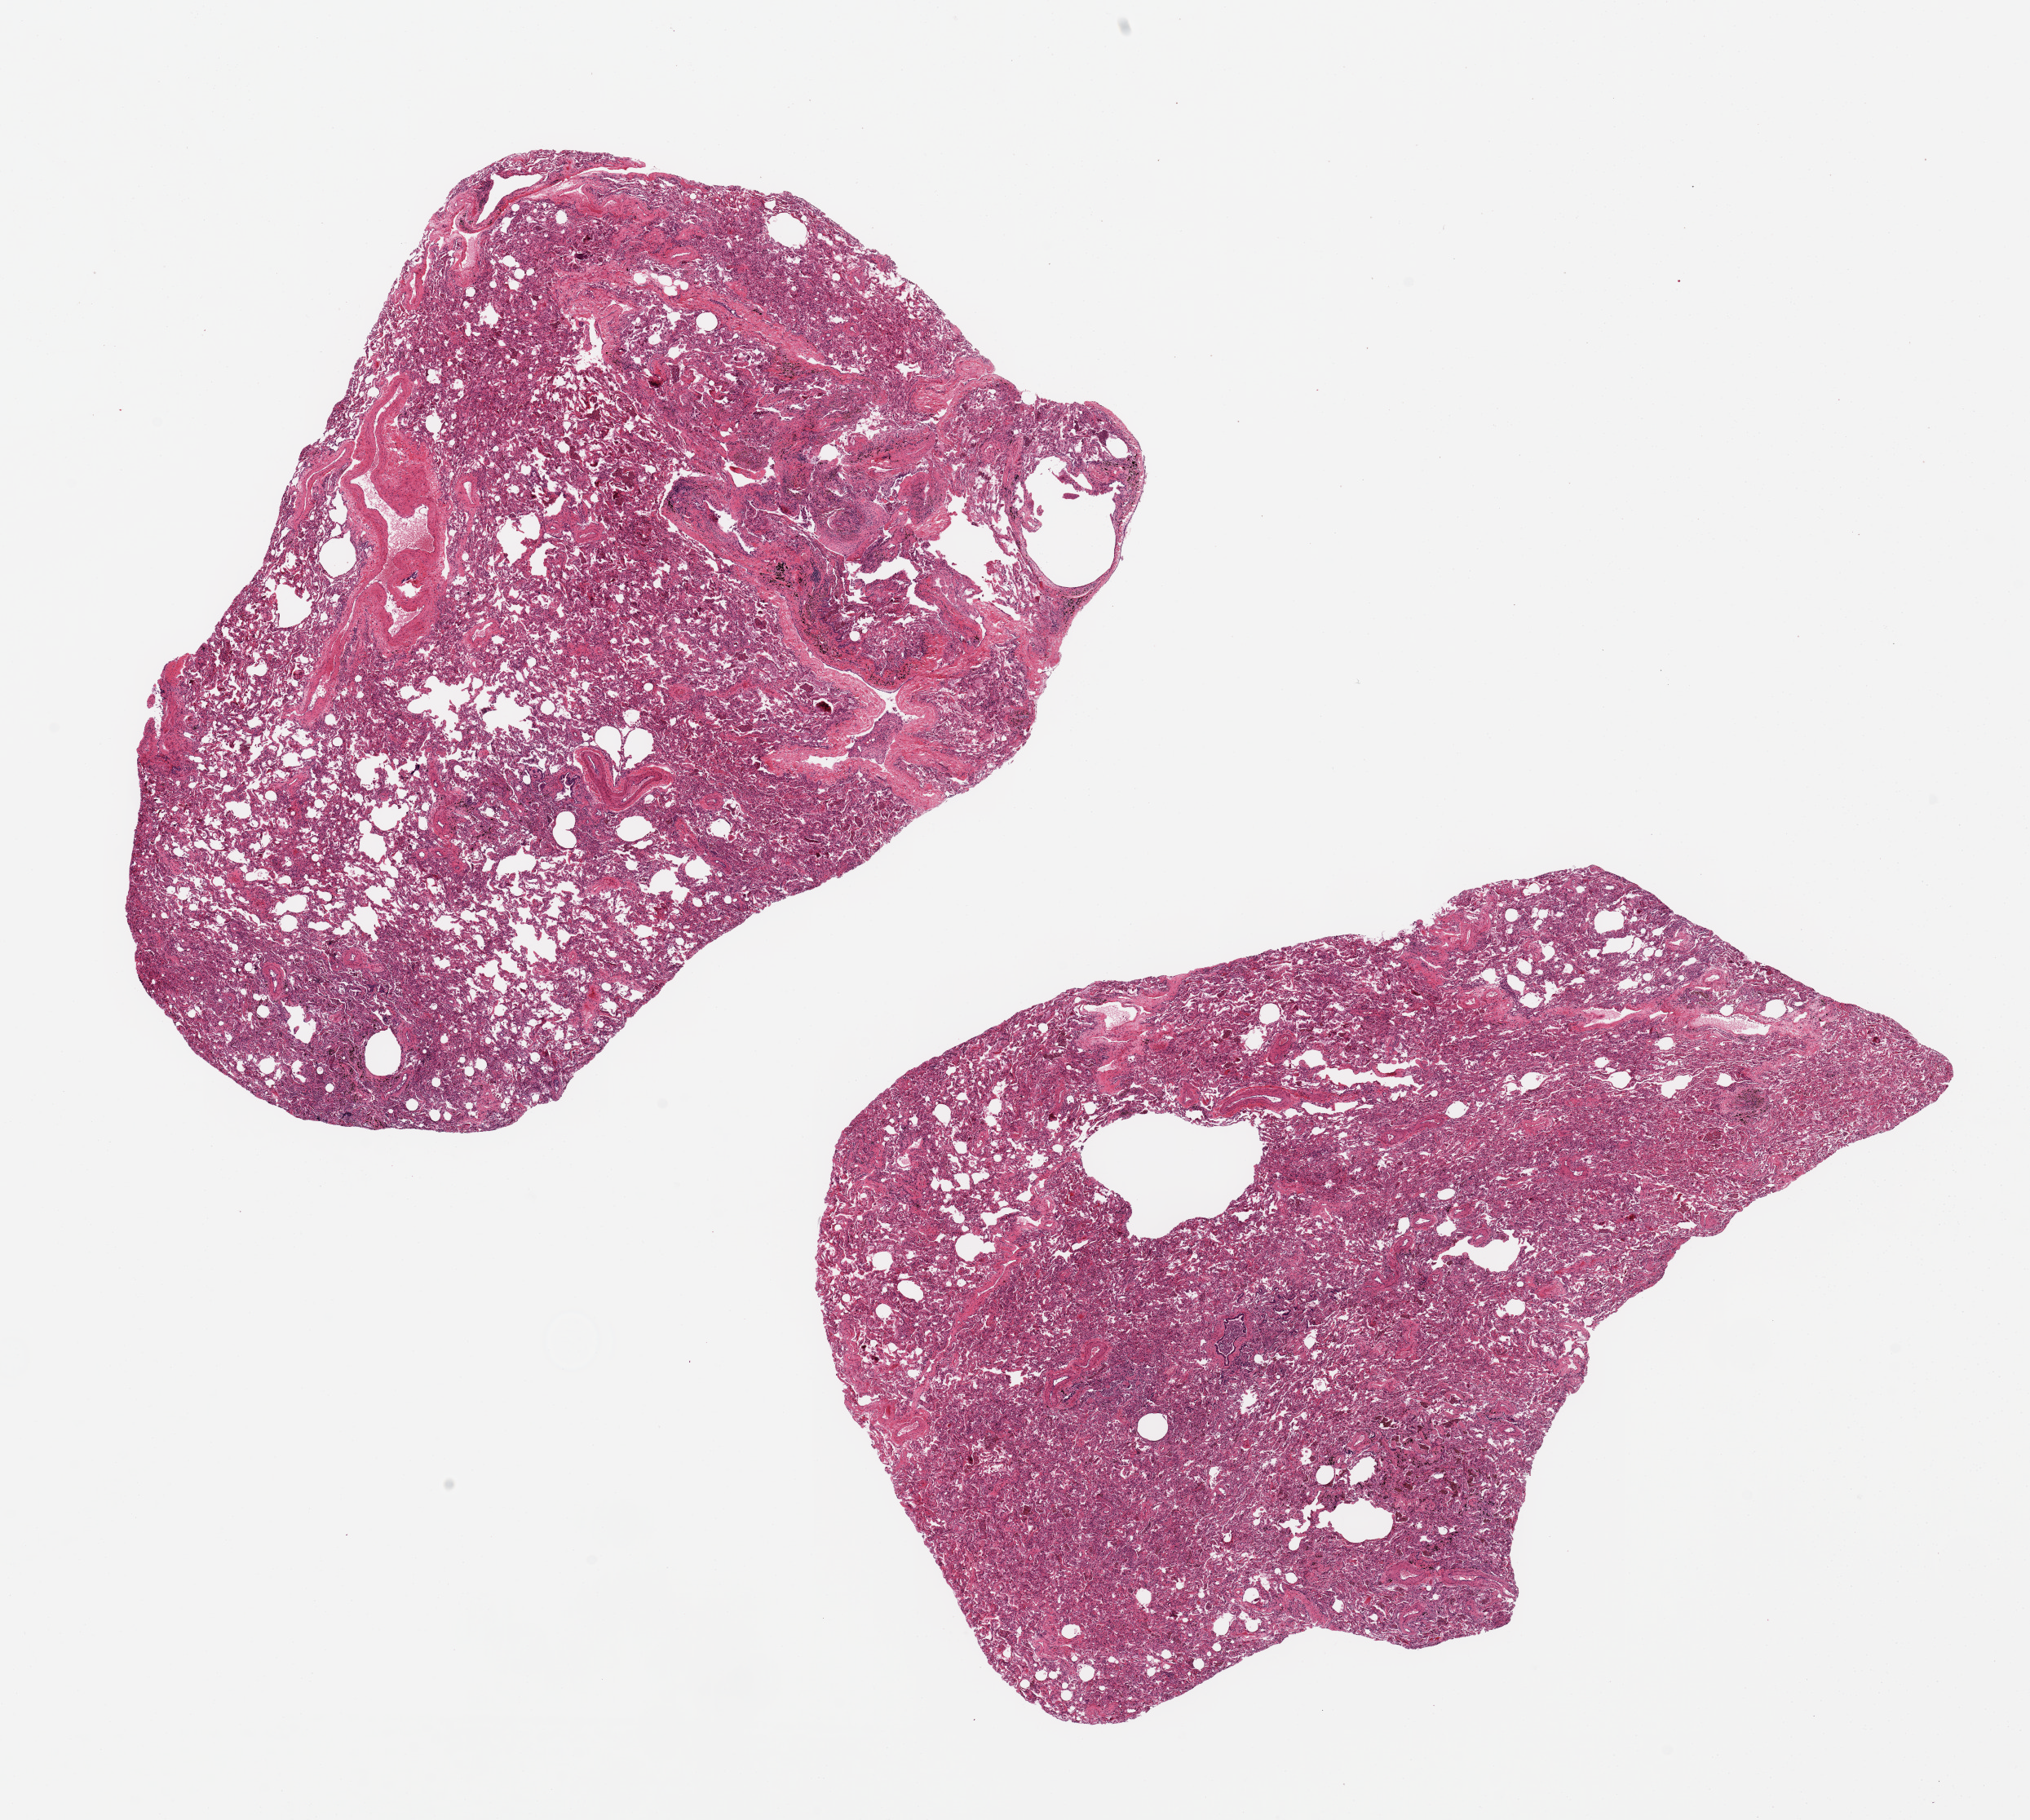
Haematoxylin and eosin whole-slide image, brightfield, shown as a low-resolution overview of the whole scanned area (about 19.7 x 17.7 mm, acquisition: 20x scan), PAXgene-fixed, paraffin-embedded tissue, section of lung (target tissue), donor tissue sample. Donor sex: male.
Review note (as recorded): 2 pieces, ~10x7 mm; patchy bronchopneumonia, ???heart failure??? cells, prominent arteries.